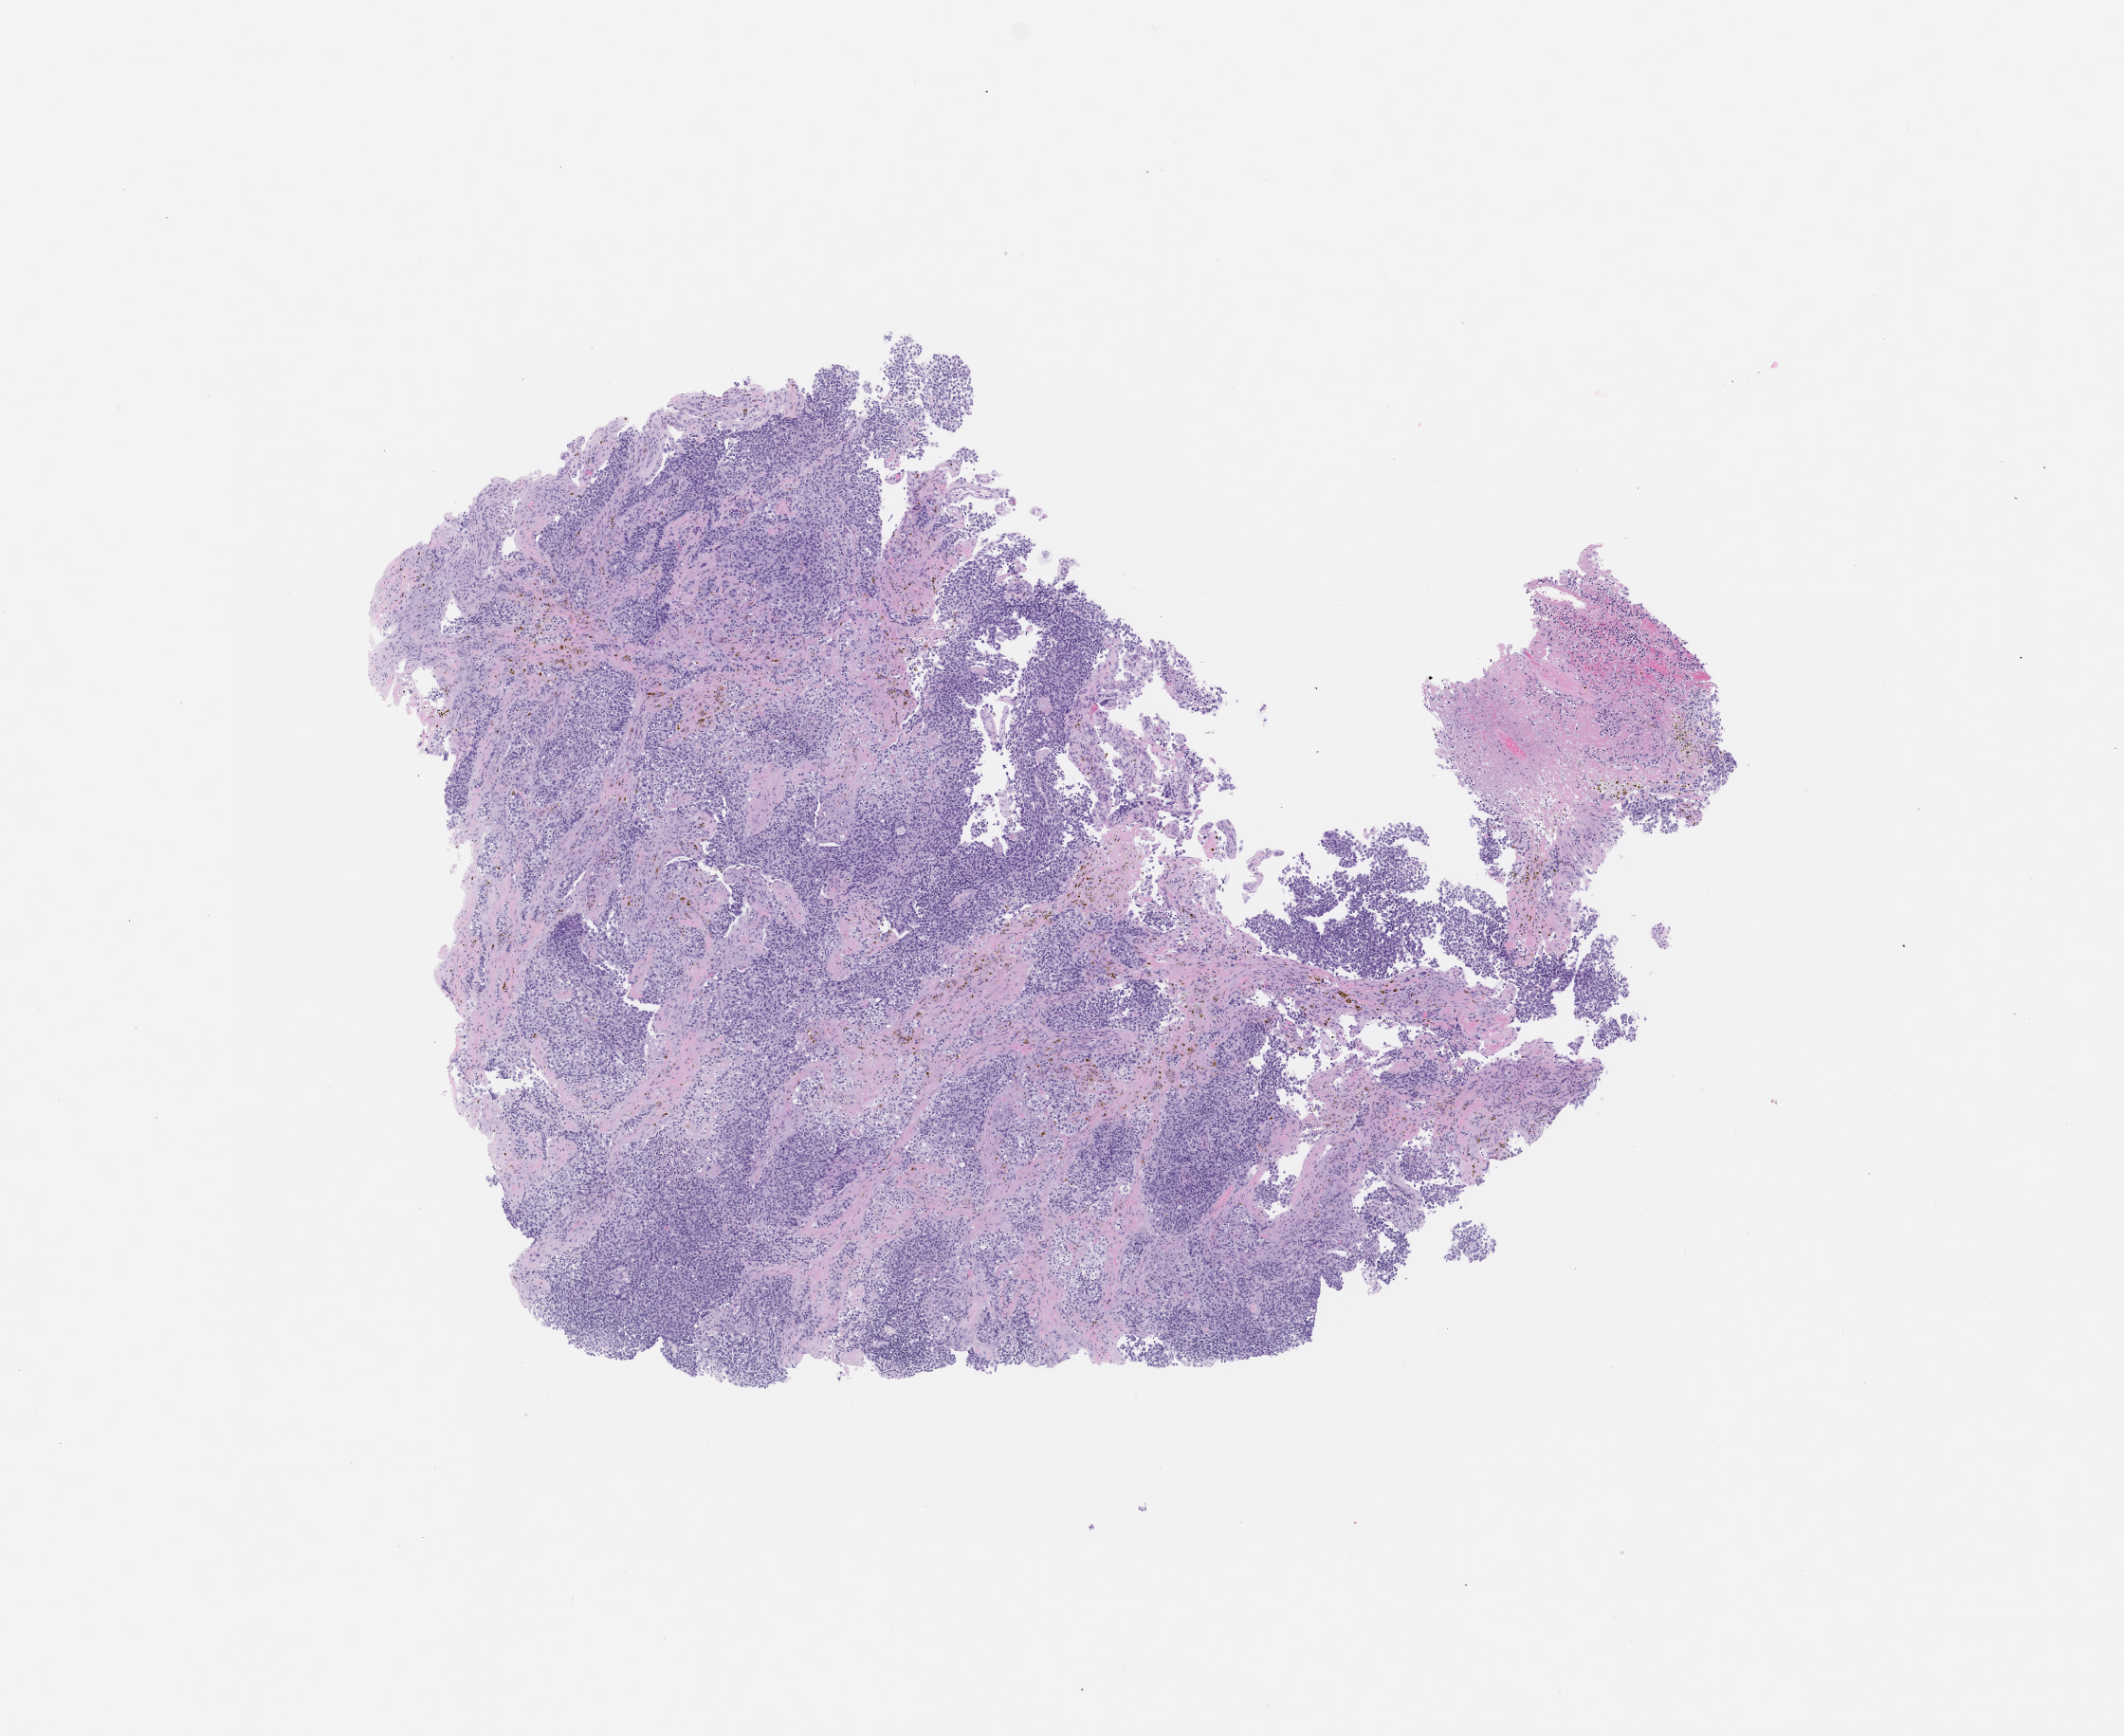
Digitized haematoxylin and eosin-stained section of the patient's (originator) tumor tissue, low-resolution overview of the scanned area, about 9.0 x 7.3 mm; formalin-fixed, paraffin-embedded (FFPE) tissue; originating tumor site category: bladder. Patient male; age 67 years.
Diagnosis: Urothelial Carcinoma.